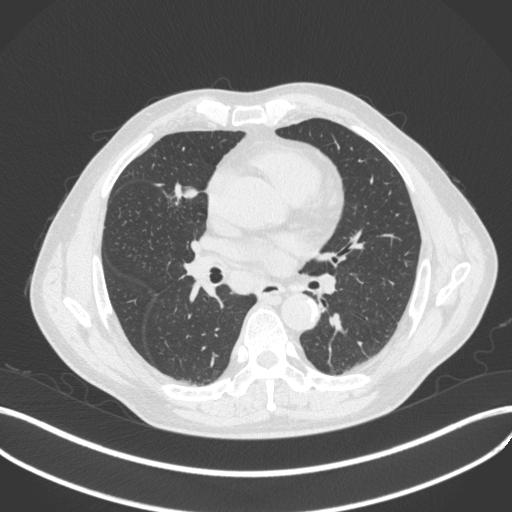
Chest CT, one axial slice; position 206 of 429 along the scan axis; reconstruction kernel B31f; 120 kVp; lung window (W 1500 / L -600 HU); 512 × 512 image matrix, field of view 400 × 400 mm. Male patient, age 61 years. From the clinical record (not read from this slice): clinical TNM (as recorded): T2b N1 M0.
Outlined on this slice (bounding box drawn by a radiologist):
- lung tumour (recorded histology: squamous cell carcinoma): bounding box [x1, y1, x2, y2] px = [168, 181, 205, 203]